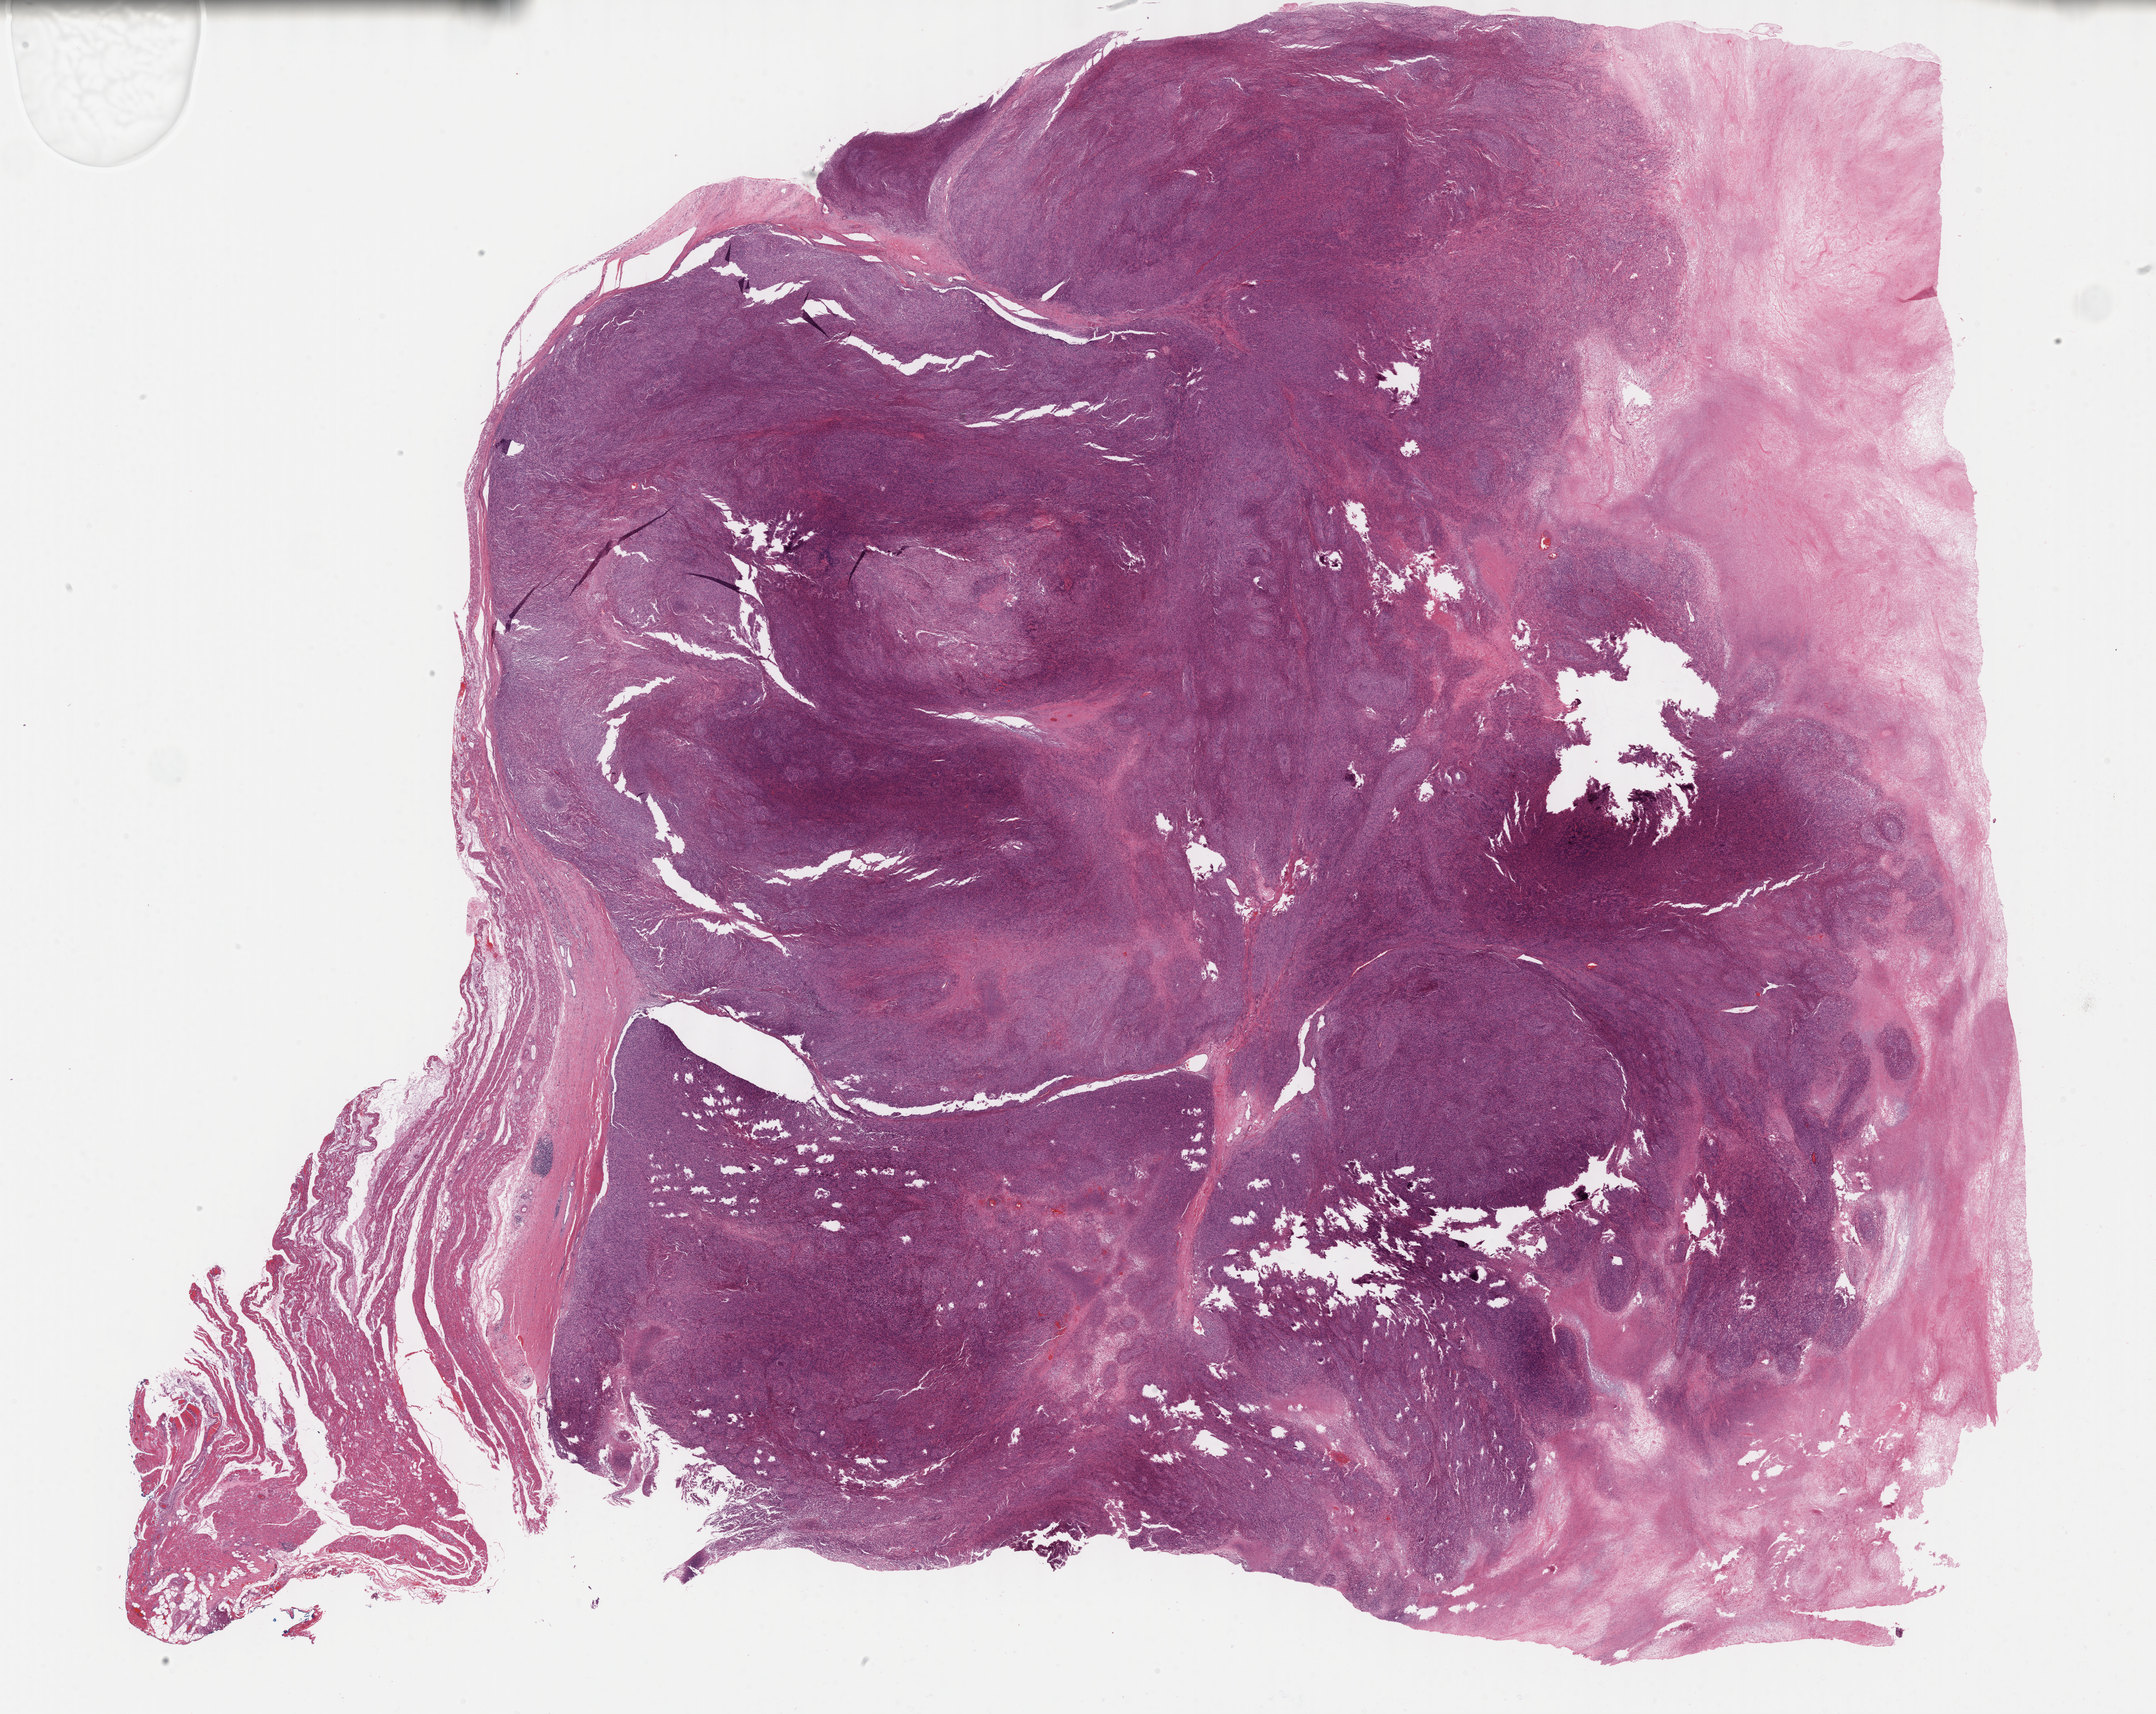
Digitized Hematoxylin and eosin (H&E) stained tissue section (whole slide), shown as a low-resolution overview of the whole scanned area (about 27.7 x 22.0 mm, from a 40x scan). Formalin-fixed paraffin-embedded (FFPE) diagnostic section. Retroperitoneum and peritoneum, primary tumour sample. Male patient; age at initial diagnosis 55 years.
• pathologic diagnosis: Undifferentiated sarcoma (retroperitoneum)